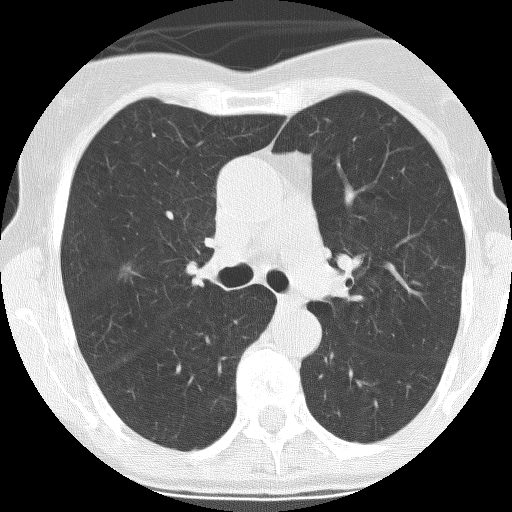
Chest CT (low-dose screening protocol), one axial image; first (baseline) screen; lung window (W 1500 / L -600 HU); 2.5 mm slice thickness; 120 kVp; slice 94 of 261 in the series. Female, age 68 years at enrolment. Former smoker at enrolment.
• Expert reader's lesion annotation, bounding box [x1, y1, x2, y2] px = [106, 246, 151, 290].
• Screening reader's record for this exam (one nodule recorded; not confirmed to be the boxed lesion): non-calcified nodule or mass ≥4 mm, right upper lobe, 13 × 8 mm, spiculated (stellate) margins, mixed attenuation.
• Later outcome: lung cancer diagnosed 113 days after this screen — adenocarcinoma, NOS, right upper lobe, moderately differentiated (G2), stage IA (AJCC 6th edition), 10 mm at pathology.